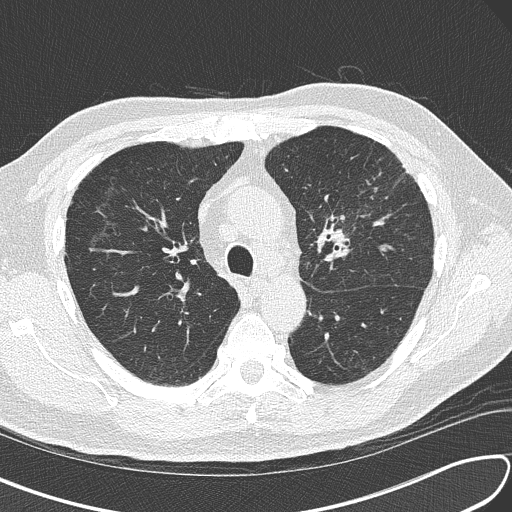
Chest CT (low-dose screening protocol), one axial image, third screening round (two years after baseline), lung window (W 1500 / L -600 HU), slice 49 of 156 in the series, 512 × 512 image matrix, field of view 340 × 340 mm. Male participant, aged 67 years at enrolment.
Expert reader's lesion annotation, bounding box <300,181,401,278> (left, top, right, bottom; pixels). The exam's reader record, not a measurement of the box and not confirmed to be the same lesion: non-calcified nodule or mass ≥4 mm, left upper lobe, 30 × 23 mm, soft tissue attenuation, pre-existing on the prior screen: no. Lung cancer was diagnosed 41 days after this screen: small cell carcinoma, NOS, left upper lobe, stage IV (AJCC 6th edition), 30 mm at pathology.